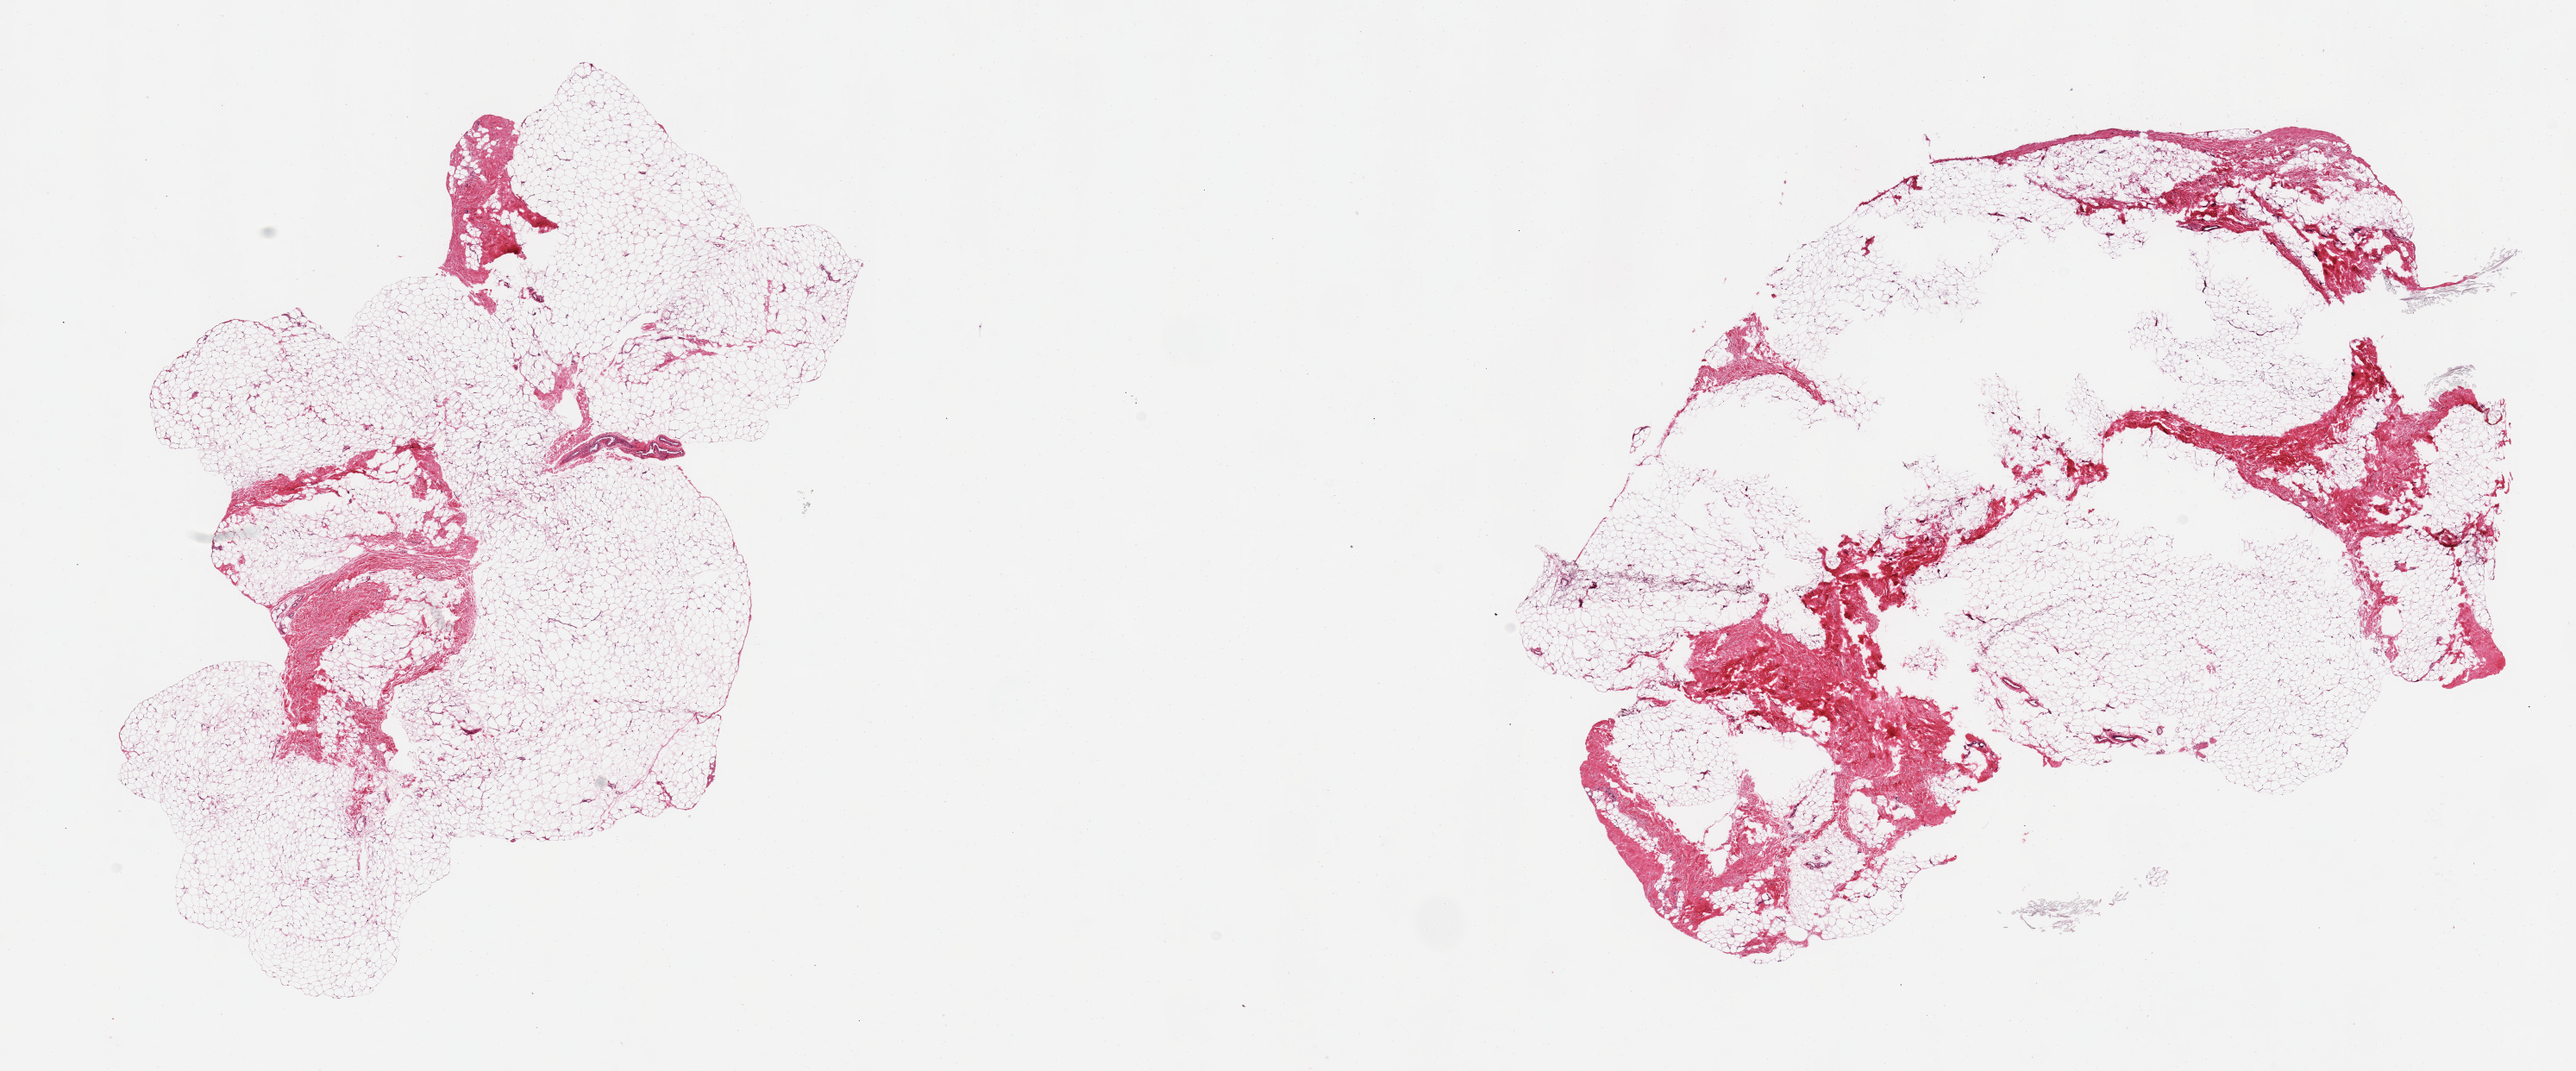
Digitized haematoxylin and eosin-stained section — low-resolution overview of the scanned area, about 23.6 x 9.8 mm, PAXgene-fixed paraffin-embedded (PFPE) section, target tissue: breast, donor tissue sample. Donor: male.
Pathologist's review note for this sample: 2 pieces; fibrofatty tissue without mammary ducts.